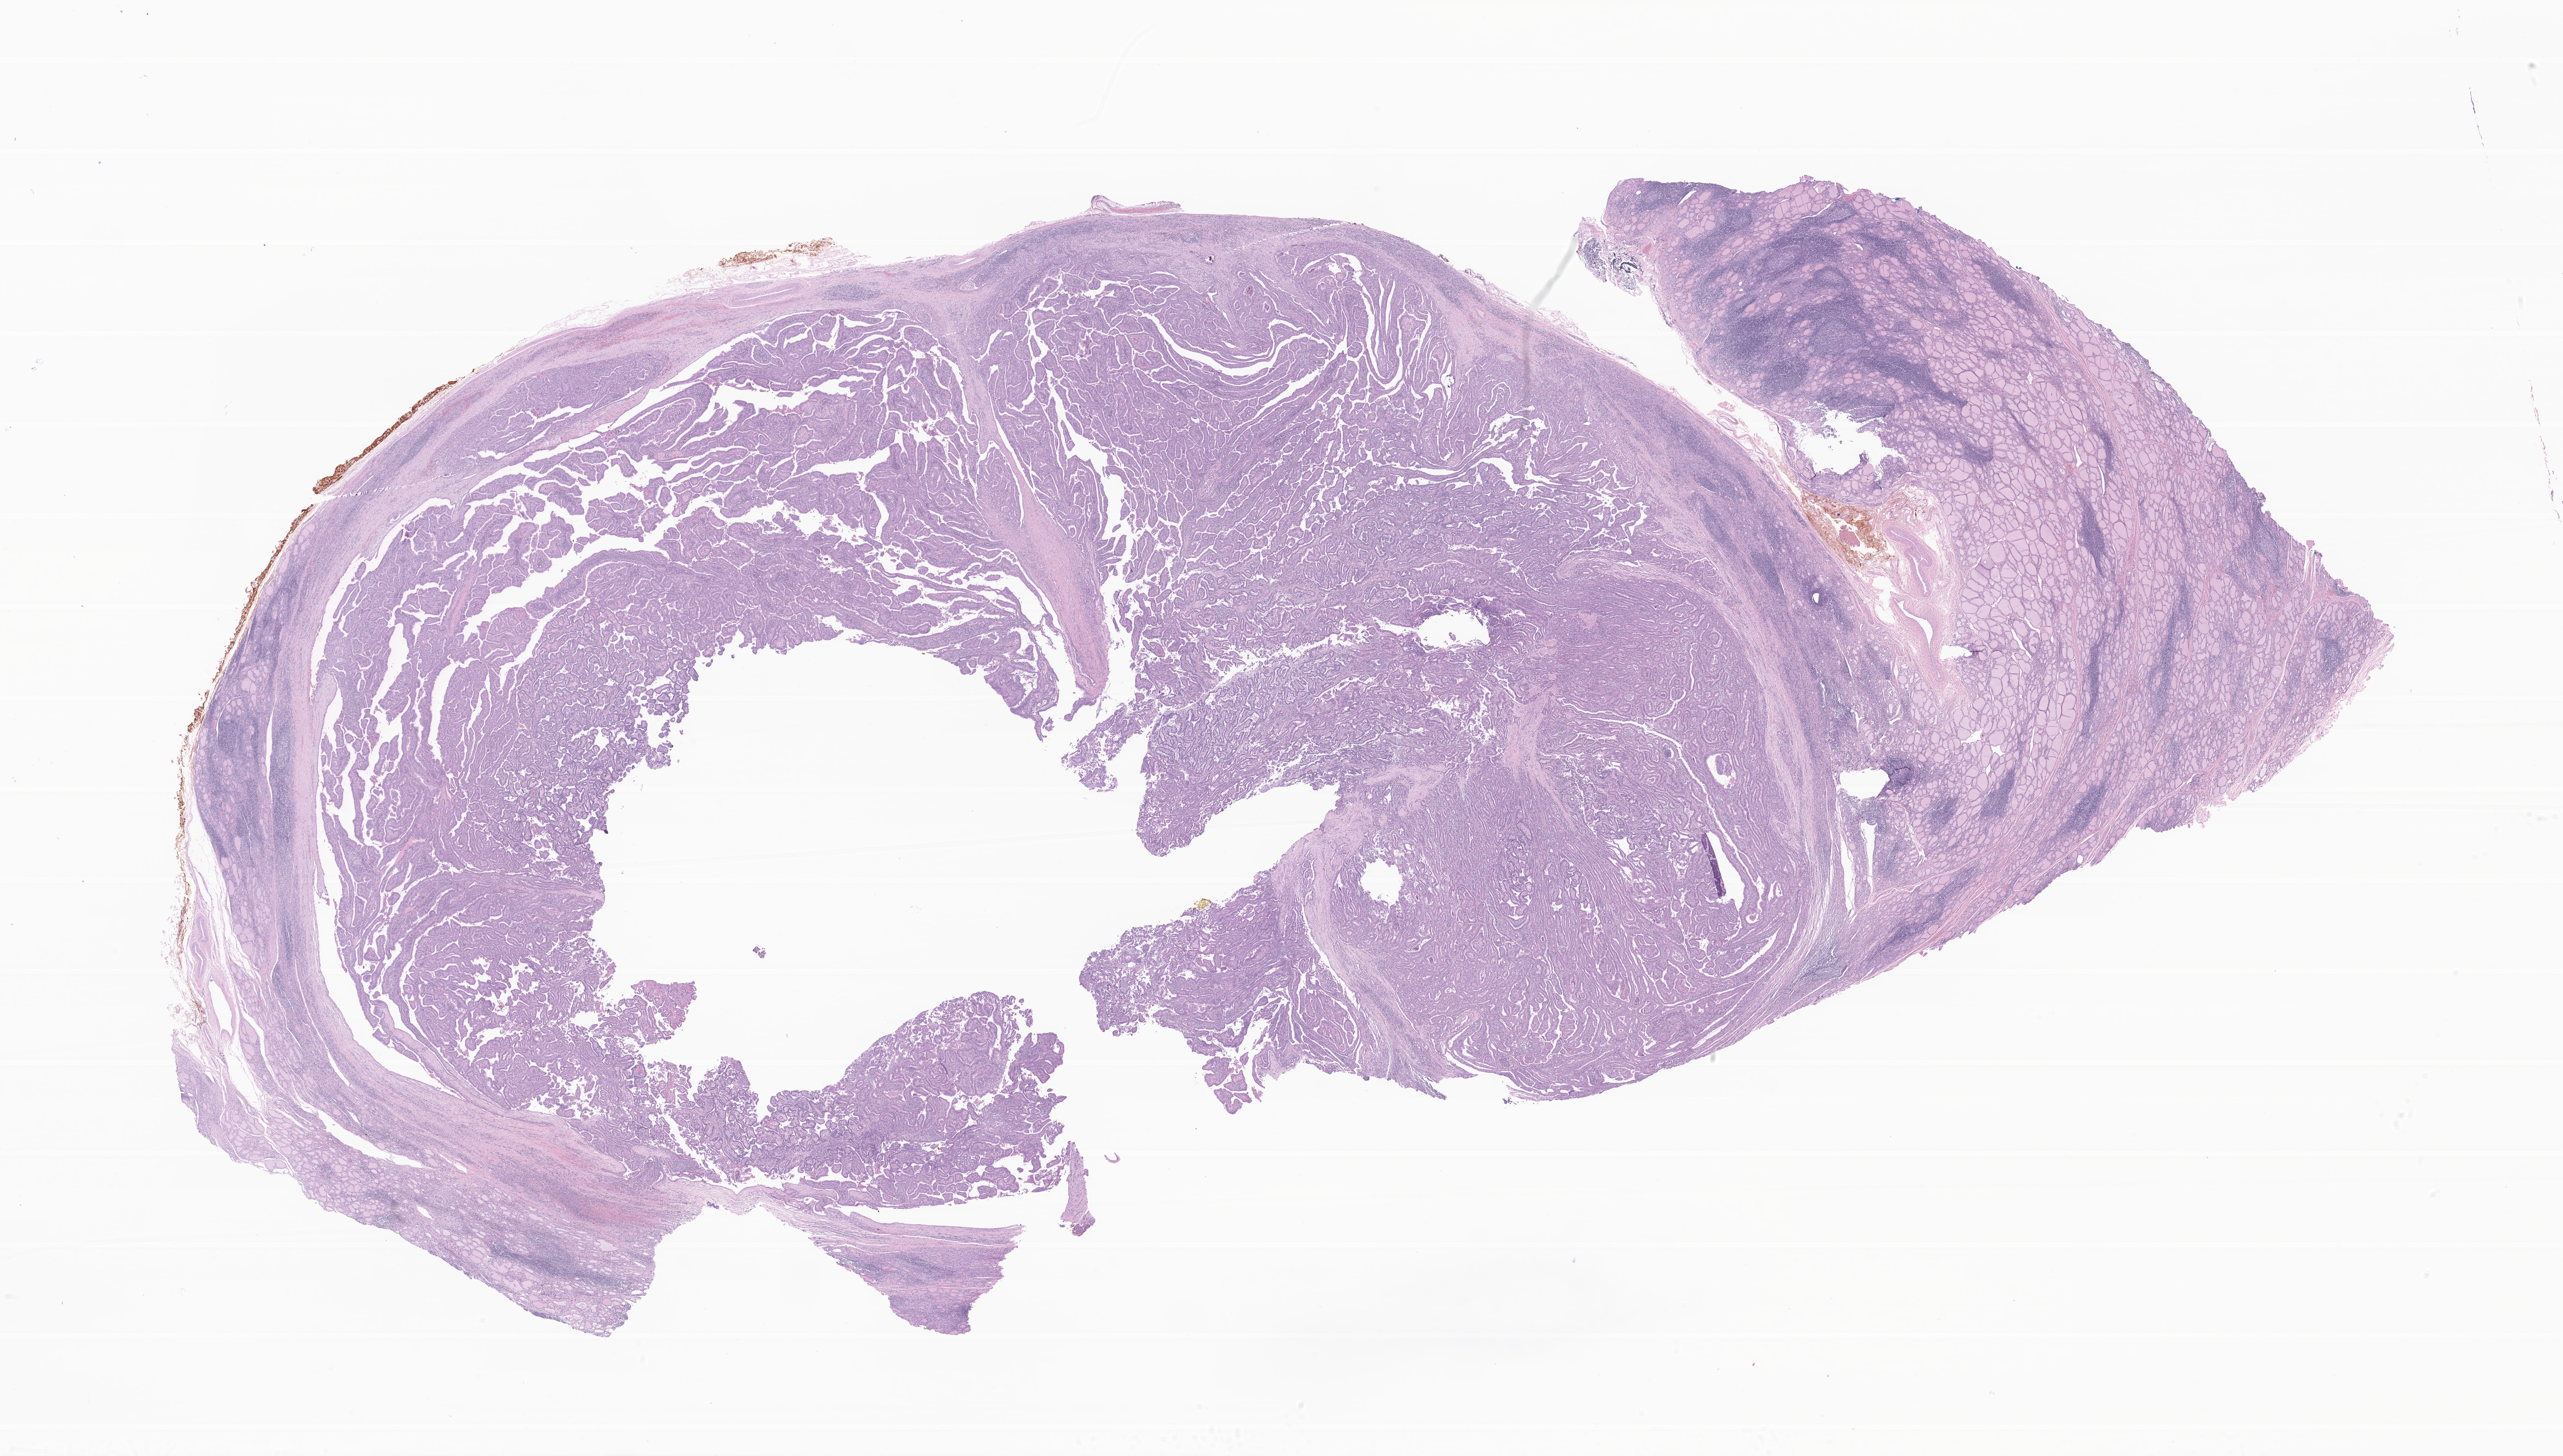
H&E whole-slide image of tumor tissue from the thyroid — shown as a low-resolution overview of the whole scanned area (about 30.0 x 17.1 mm), formalin-fixed, paraffin-embedded (FFPE) tissue. Female patient, age 183 months (15 years 3 months).
Diagnosis (ICD-O-3 morphology term): Papillary adenocarcinoma, NOS.